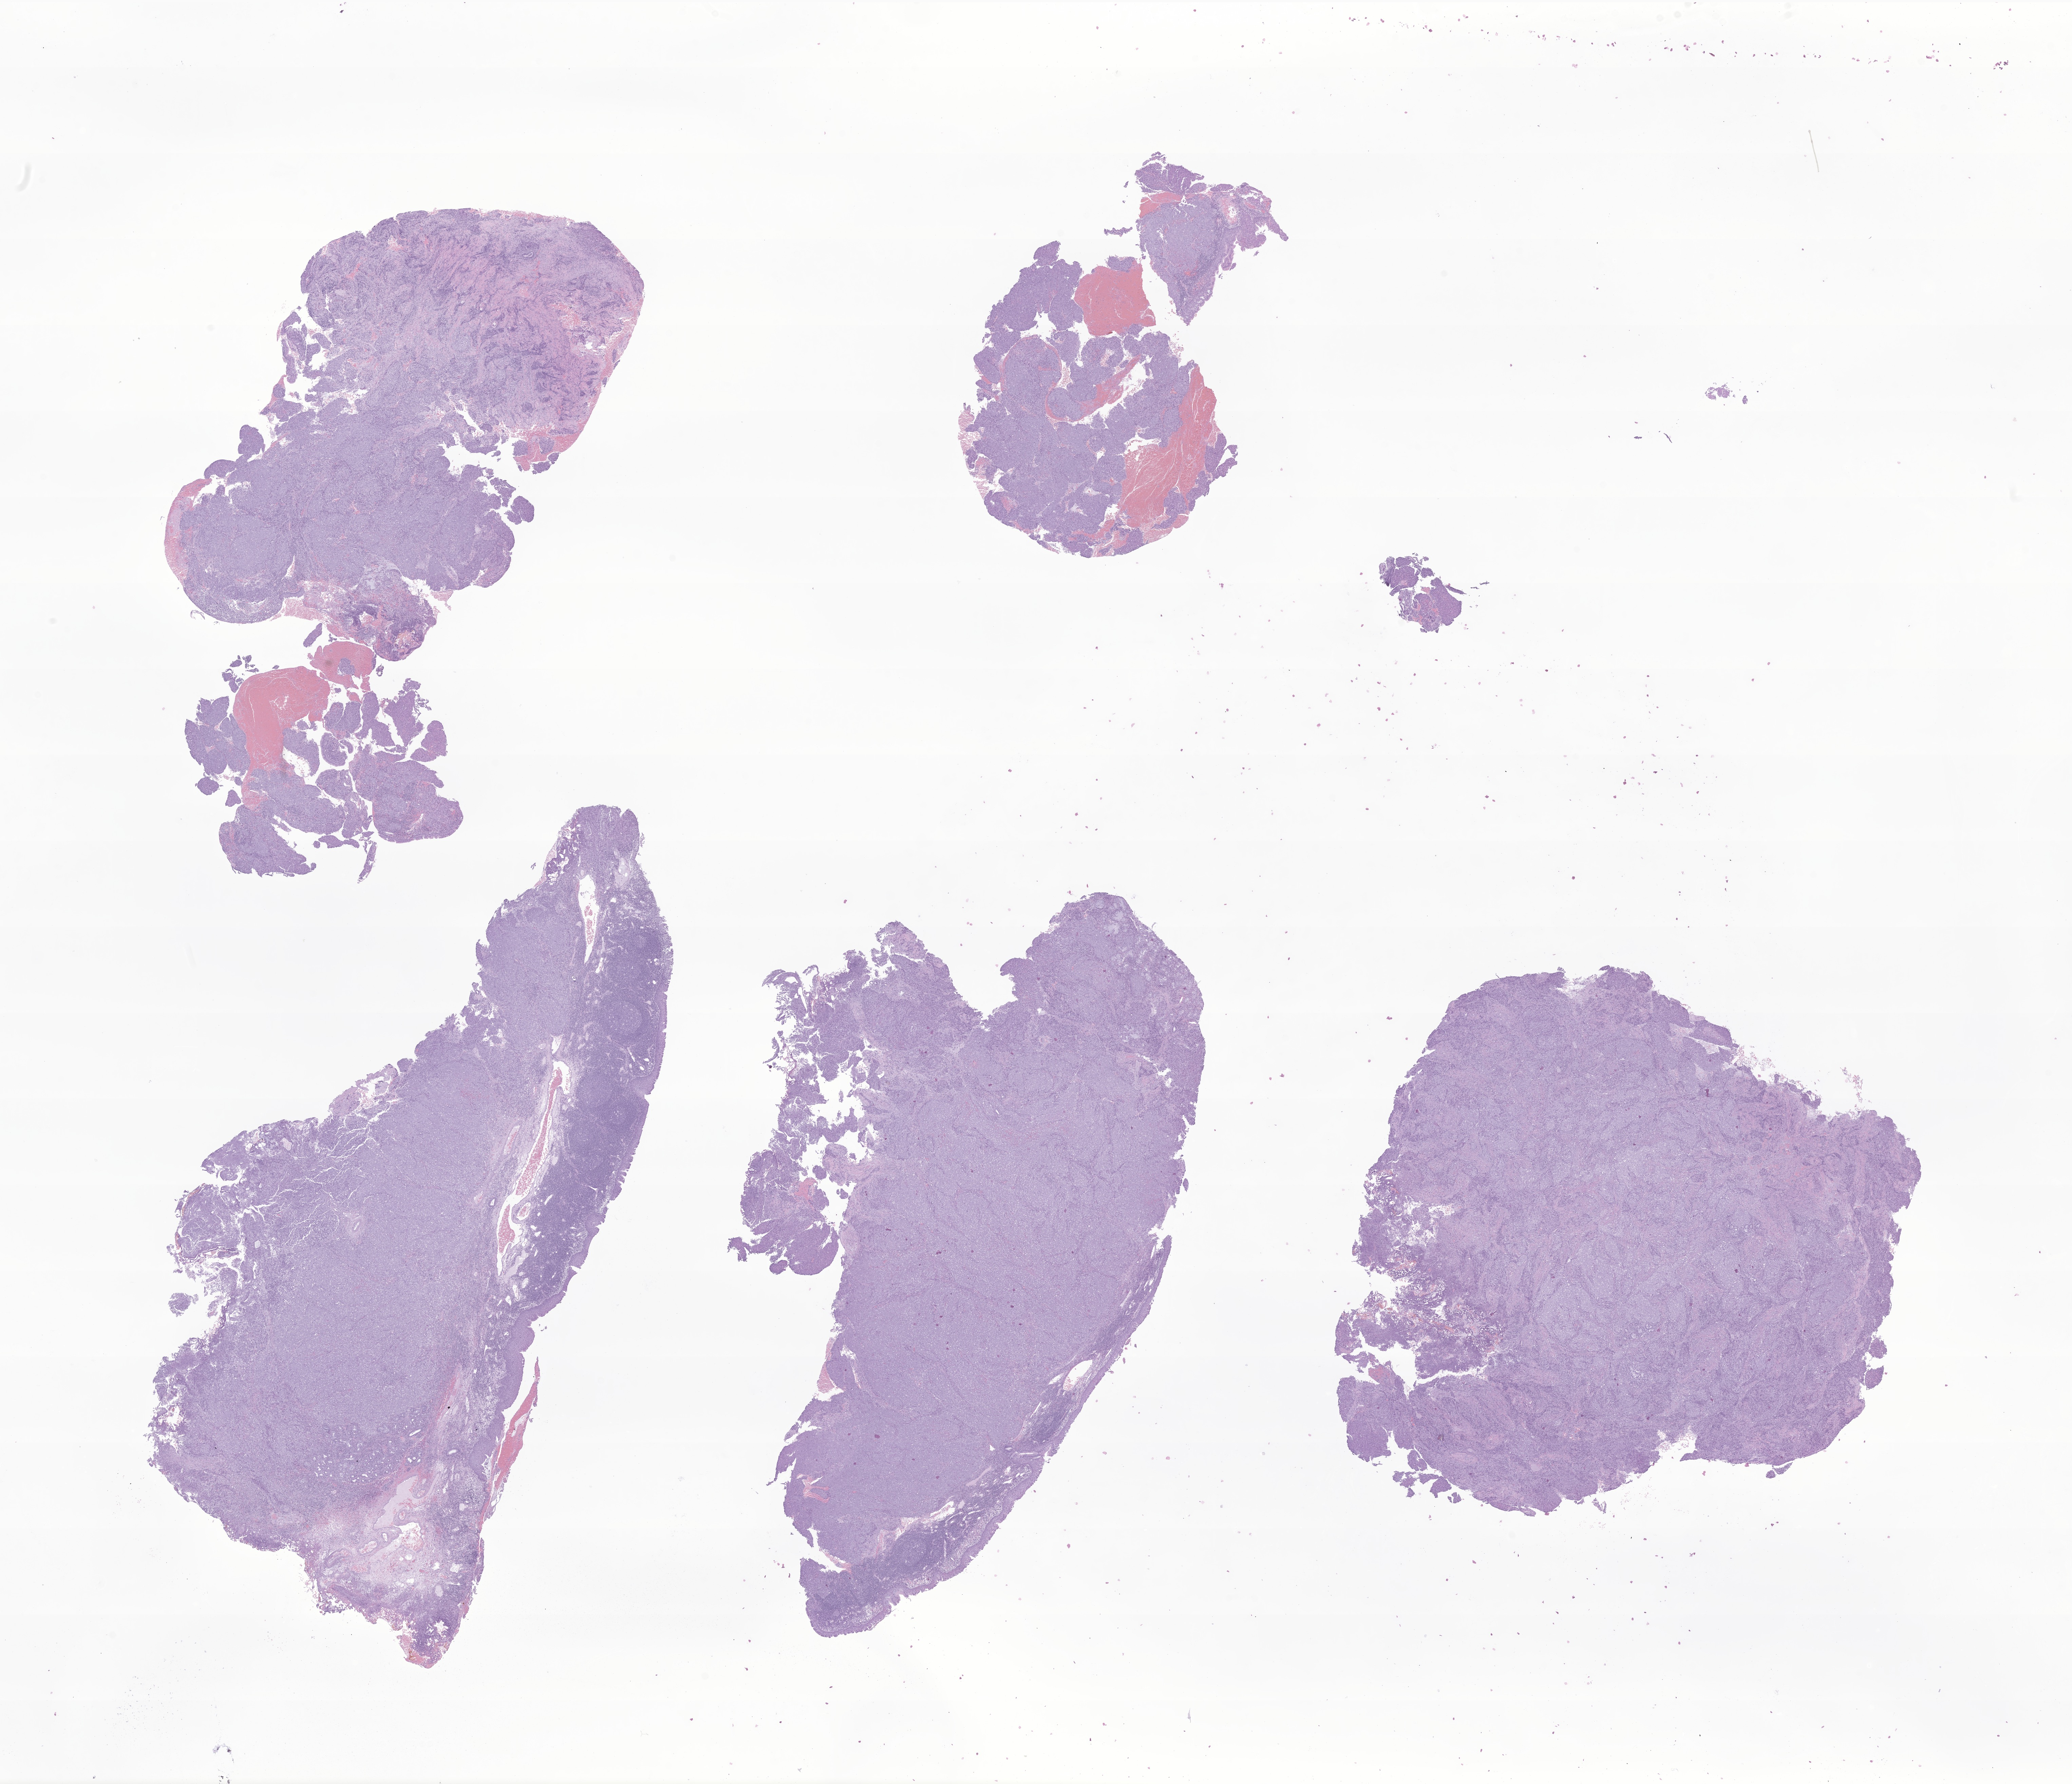
Whole-slide image, haematoxylin and eosin stain of tumor tissue from the nasopharynx — whole scanned area (about 25.7 x 22.2 mm) shown as a low-resolution overview. FFPE section. Patient: male, age 142 months (11 years 10 months).
- recorded diagnosis: Squamous cell carcinoma, large cell, nonkeratinizing, NOS